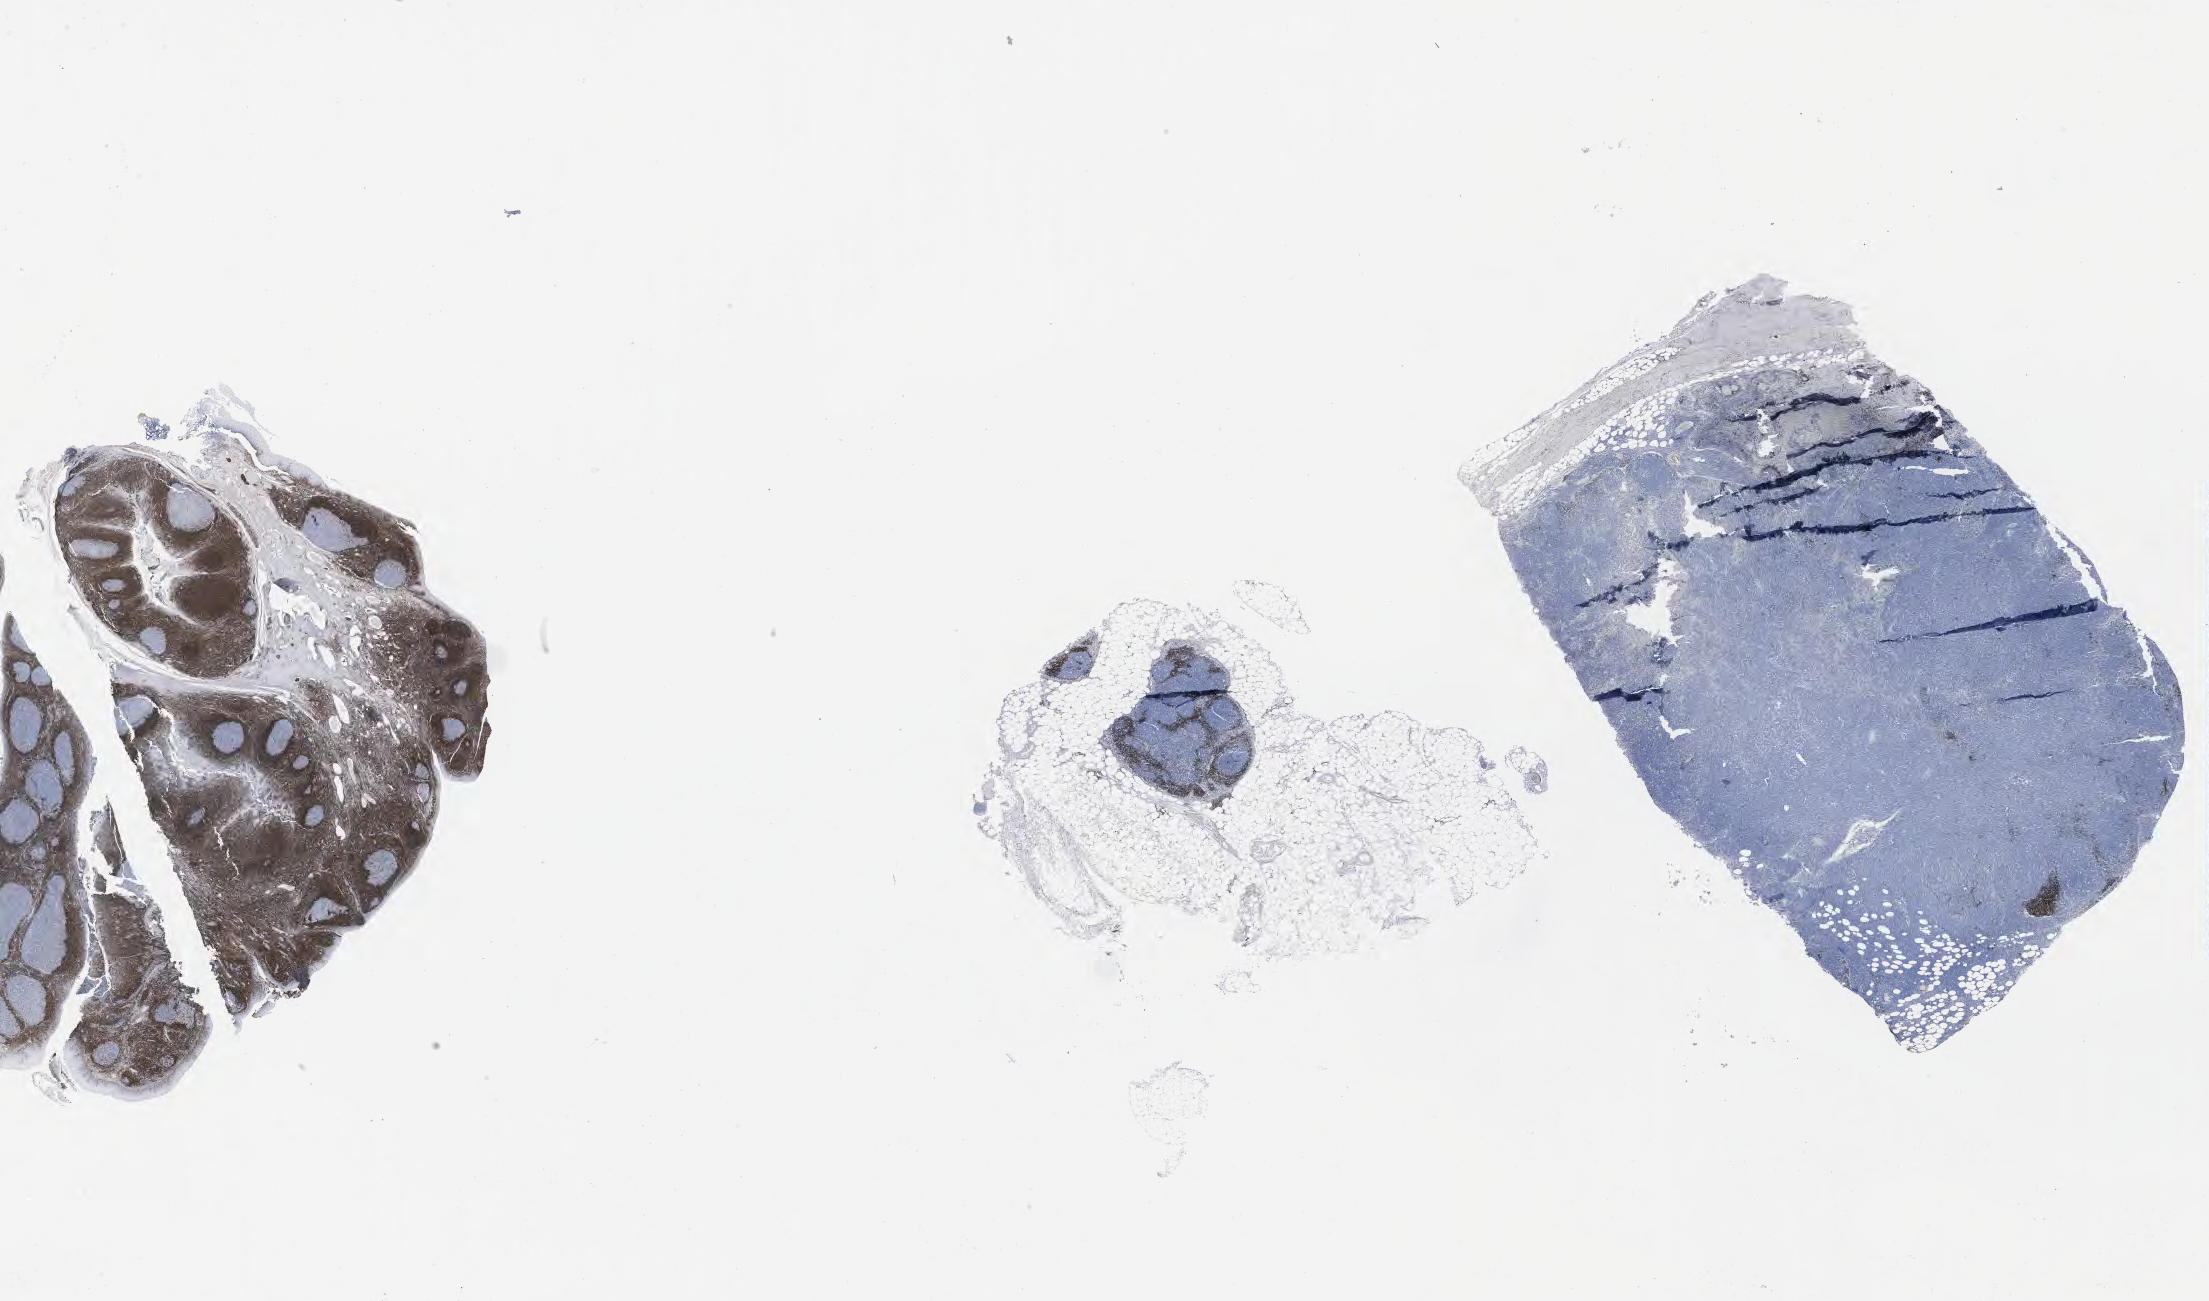
Immunohistochemistry (IHC) whole-slide image stained for BCL2, low-resolution overview of the scanned area, about 35.7 x 21.0 mm. Tumor tissue. Male patient, age 40 years.
- histologic diagnosis: Burkitt lymphoma, NOS